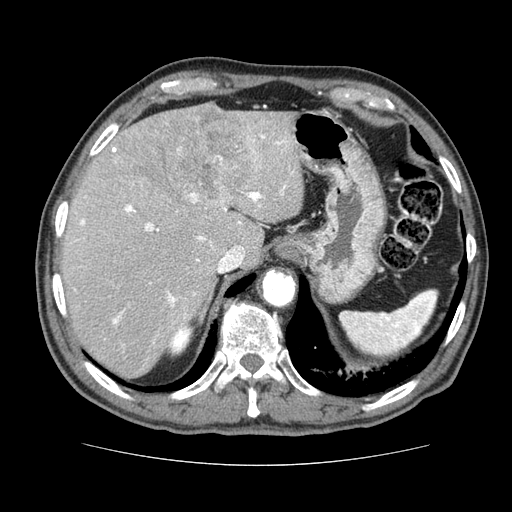
Contrast-enhanced abdominal CT (liver protocol), one axial slice. Slice 55 of 79 in the series (ordered by position). Soft-tissue window (W 400 / L 40 HU). 512 × 512 image matrix. Case-level facts recorded for this patient, not image findings: diagnosis: hepatocellular carcinoma (patient treated with transarterial chemoembolisation; whether this scan precedes or follows treatment is not stated here); TNM stage (as recorded): Stage-I; Child-Pugh class: A.
Outlined on this slice (semi-automatically segmented with operator editing):
- liver parenchyma outside the tumour (the mass and vessels are separate outlines, so this box may not span the whole liver): bounding box <60,102,304,378> (left, top, right, bottom; pixels)
- mass: <149,103,252,206>
- liver vessels: <76,134,293,324>